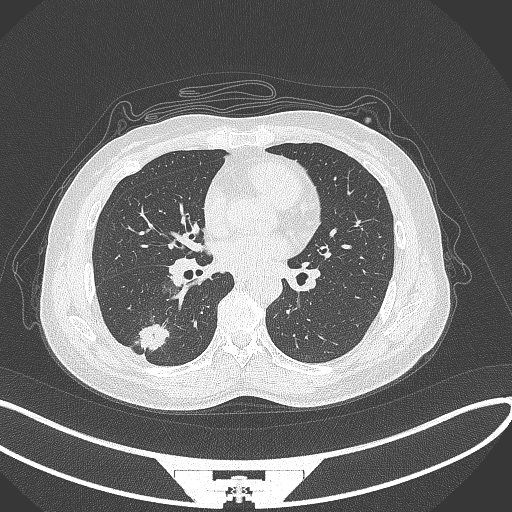
Chest CT, one axial slice; position 140 of 352 along the scan axis; reconstruction kernel B70f; 120 kVp; lung window (W 1500 / L -600 HU); 1 mm slice thickness; 512 × 512 image matrix, field of view 400 × 400 mm. Patient: female, 55 years. From the clinical record (not read from this slice): clinical TNM (as recorded): T1c N1 M0.
Structures marked on this image (rectangle marked by the reading radiologist):
- lung tumour (recorded histology: adenocarcinoma): bounding box [x1, y1, x2, y2] px = [134, 317, 176, 360]